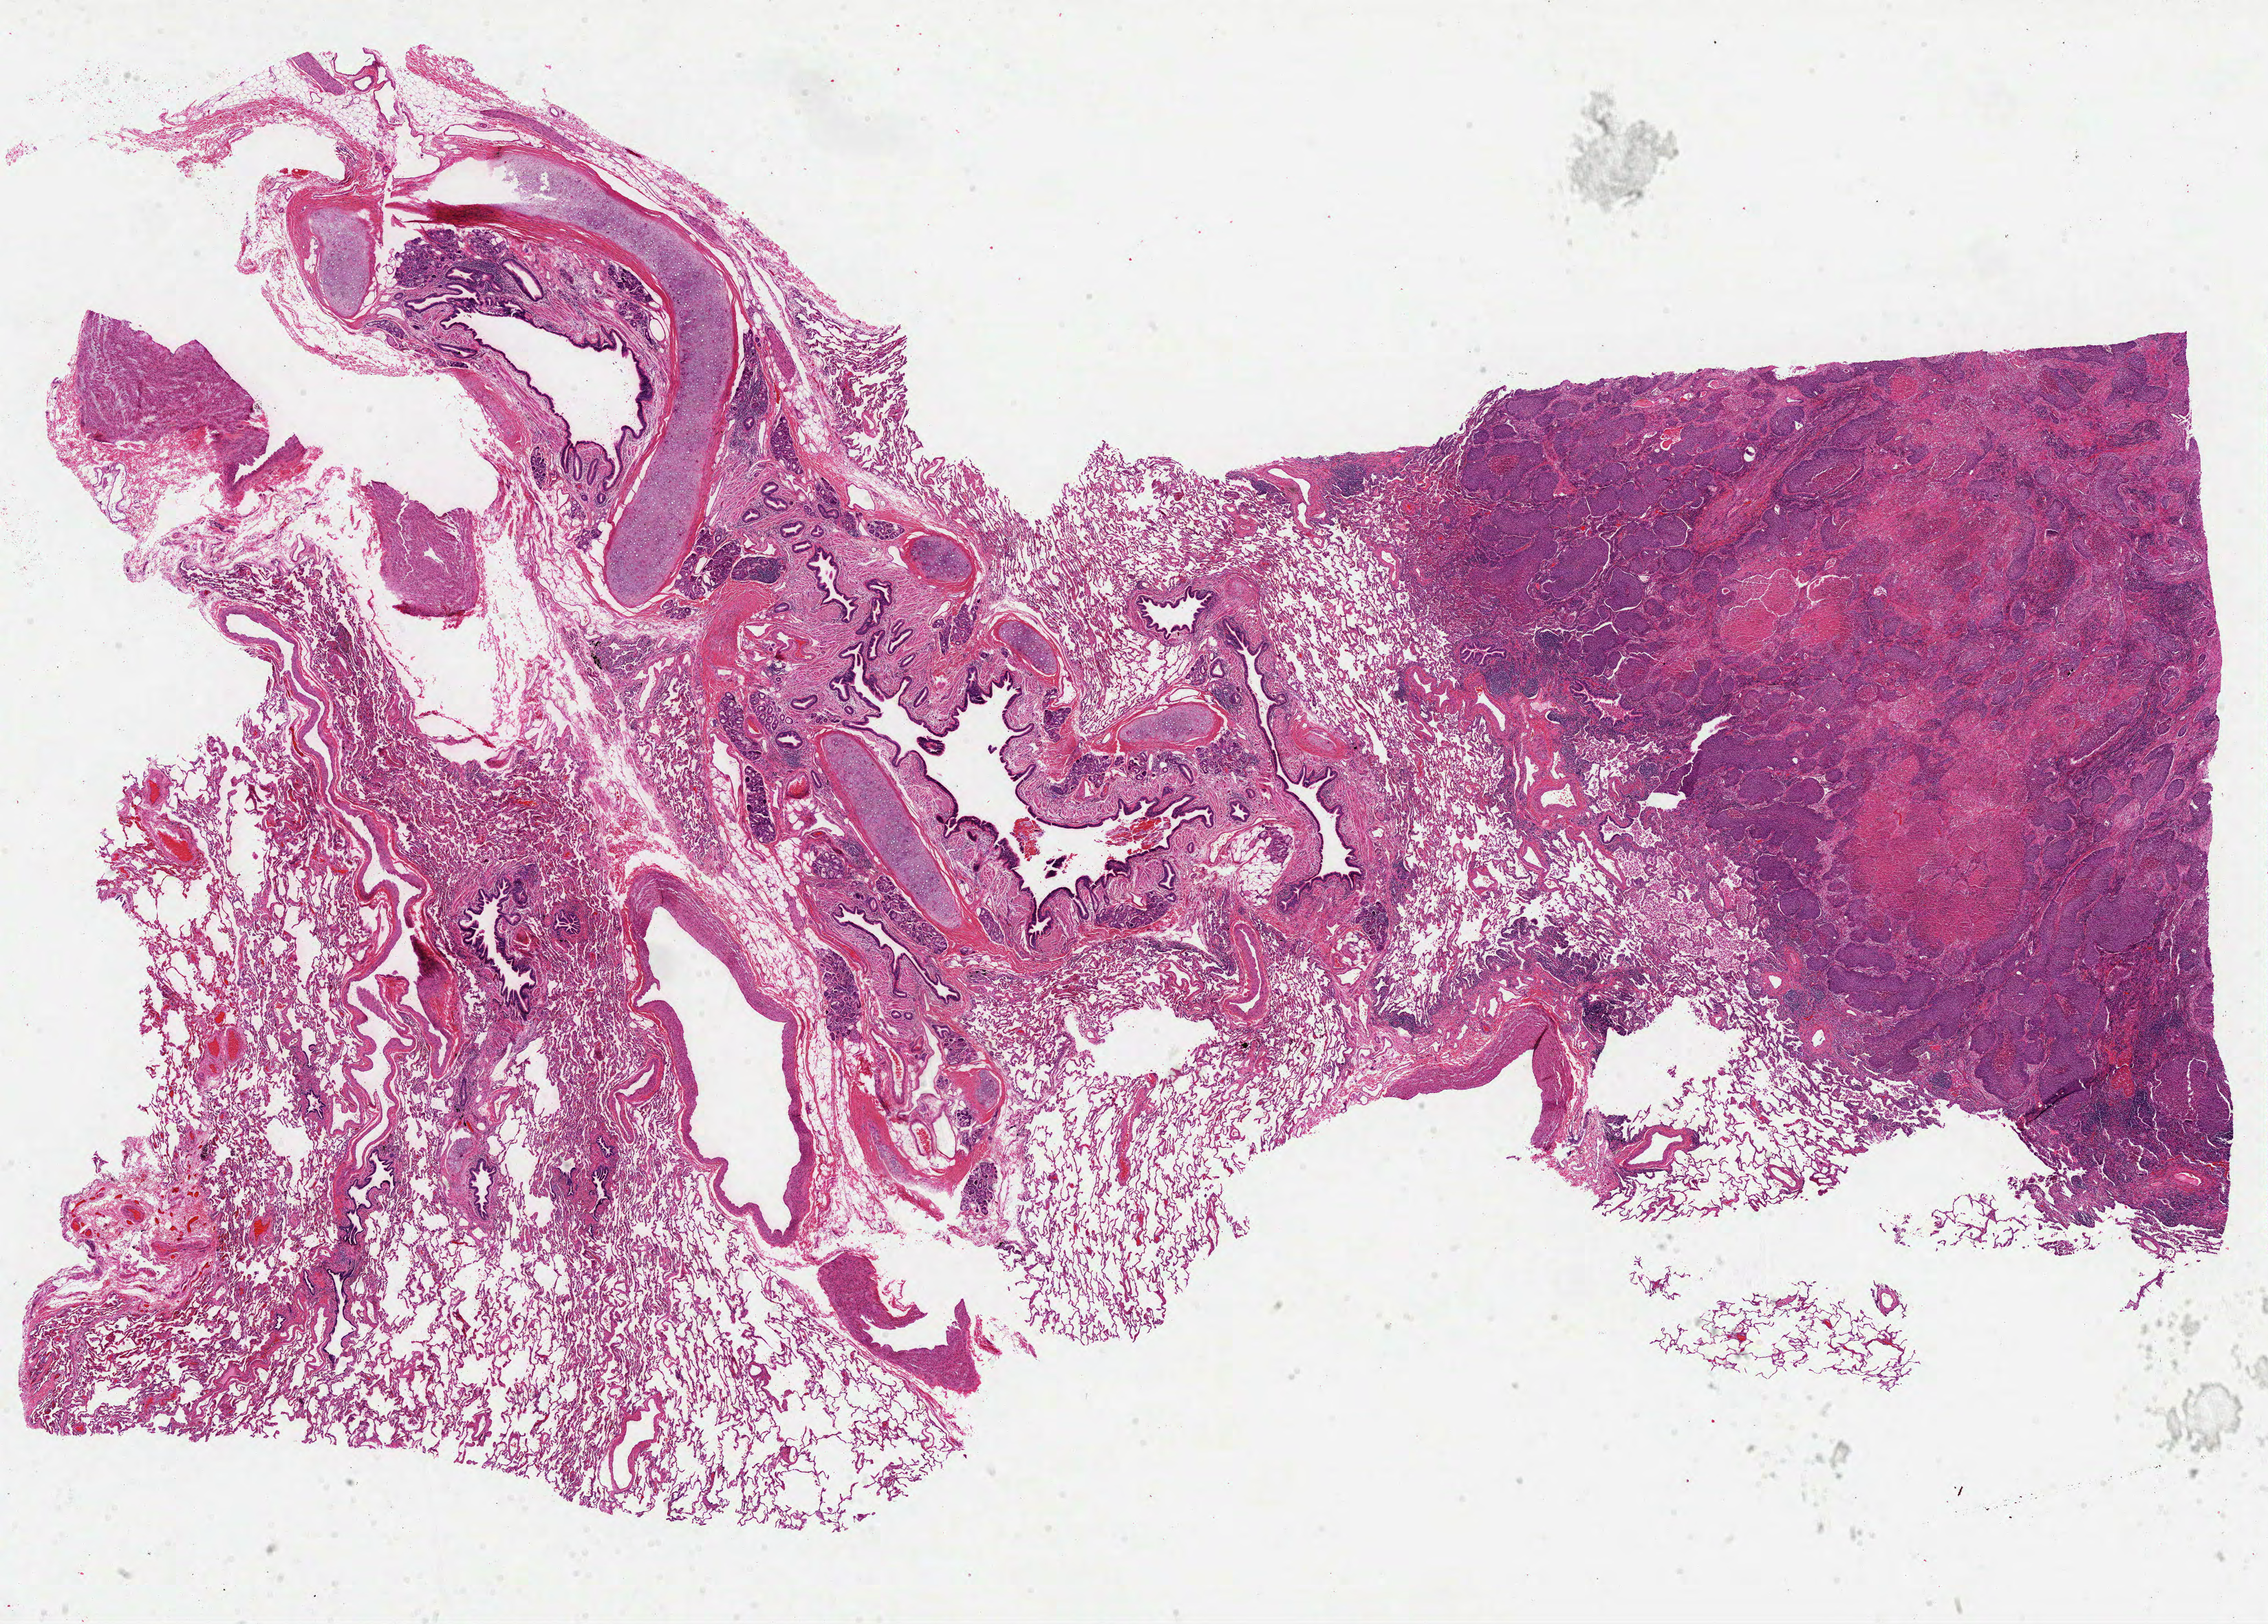
Whole-slide histology image, H&E, shown as a low-resolution overview of the whole scanned area (about 26.6 x 19.0 mm), FFPE section, sample: primary tumour, lung. Male patient; age at initial diagnosis 68 years.
AJCC pathologic stage: IB (6th edition). Histologic diagnosis: Squamous cell carcinoma, NOS (upper lobe, lung).